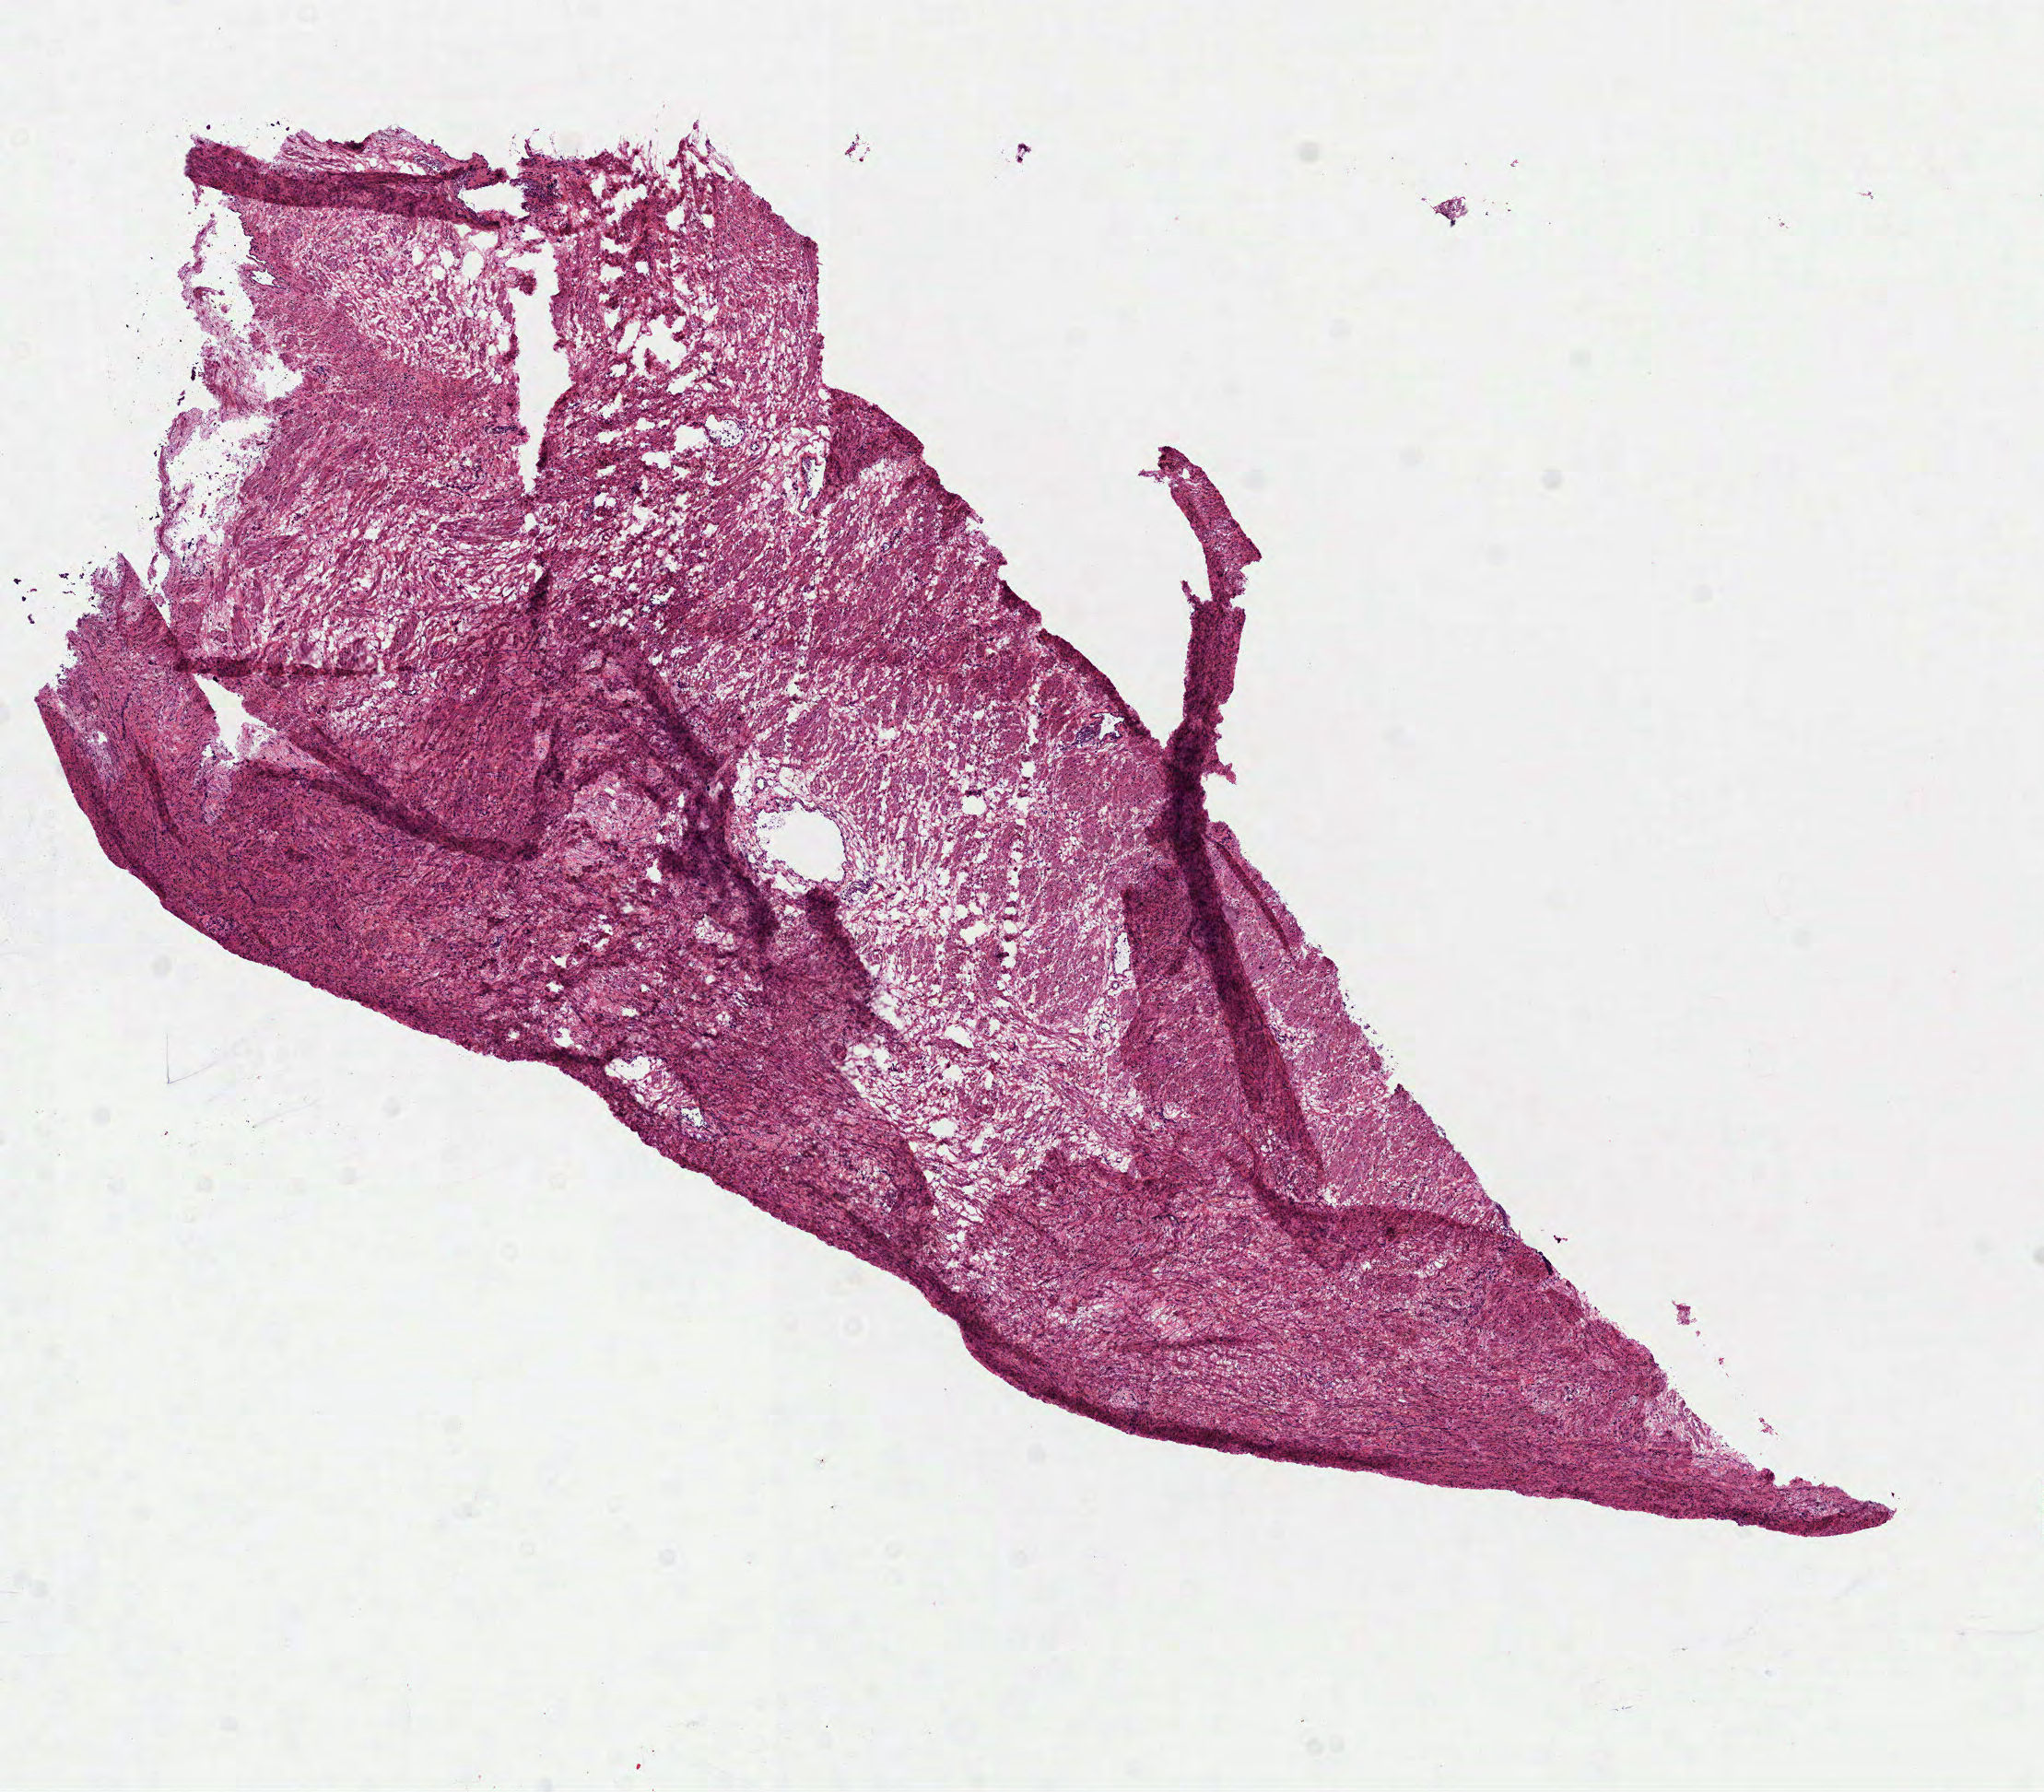
Whole-slide histology image, H&E-stained — whole scanned area (about 8.9 x 7.8 mm, slide scanned at 40x) shown as a low-resolution overview; frozen section; solid tissue normal (non-tumour tissue) sample from the prostate. Patient: male, age at initial diagnosis 60 years.
This section: solid tissue normal (non-tumour) sample from the same patient. Patient diagnosis: Acinar cell carcinoma (prostate gland).